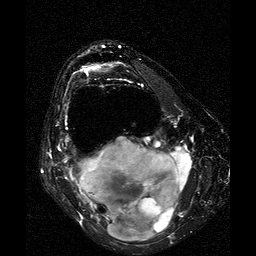
MRI of an extremity soft-tissue mass, one axial slice; slice 15 of 25 in the series (ordered by position); T2-weighted fat-saturated; 256 × 256 image matrix. Female patient. From the clinical record (not read from this slice): histological type: liposarcoma; site of the primary tumour: right thigh.
Structures marked on this image (expert manual segmentation):
- gross tumour volume (mass): box from (x=72, y=137) to (x=192, y=243) px